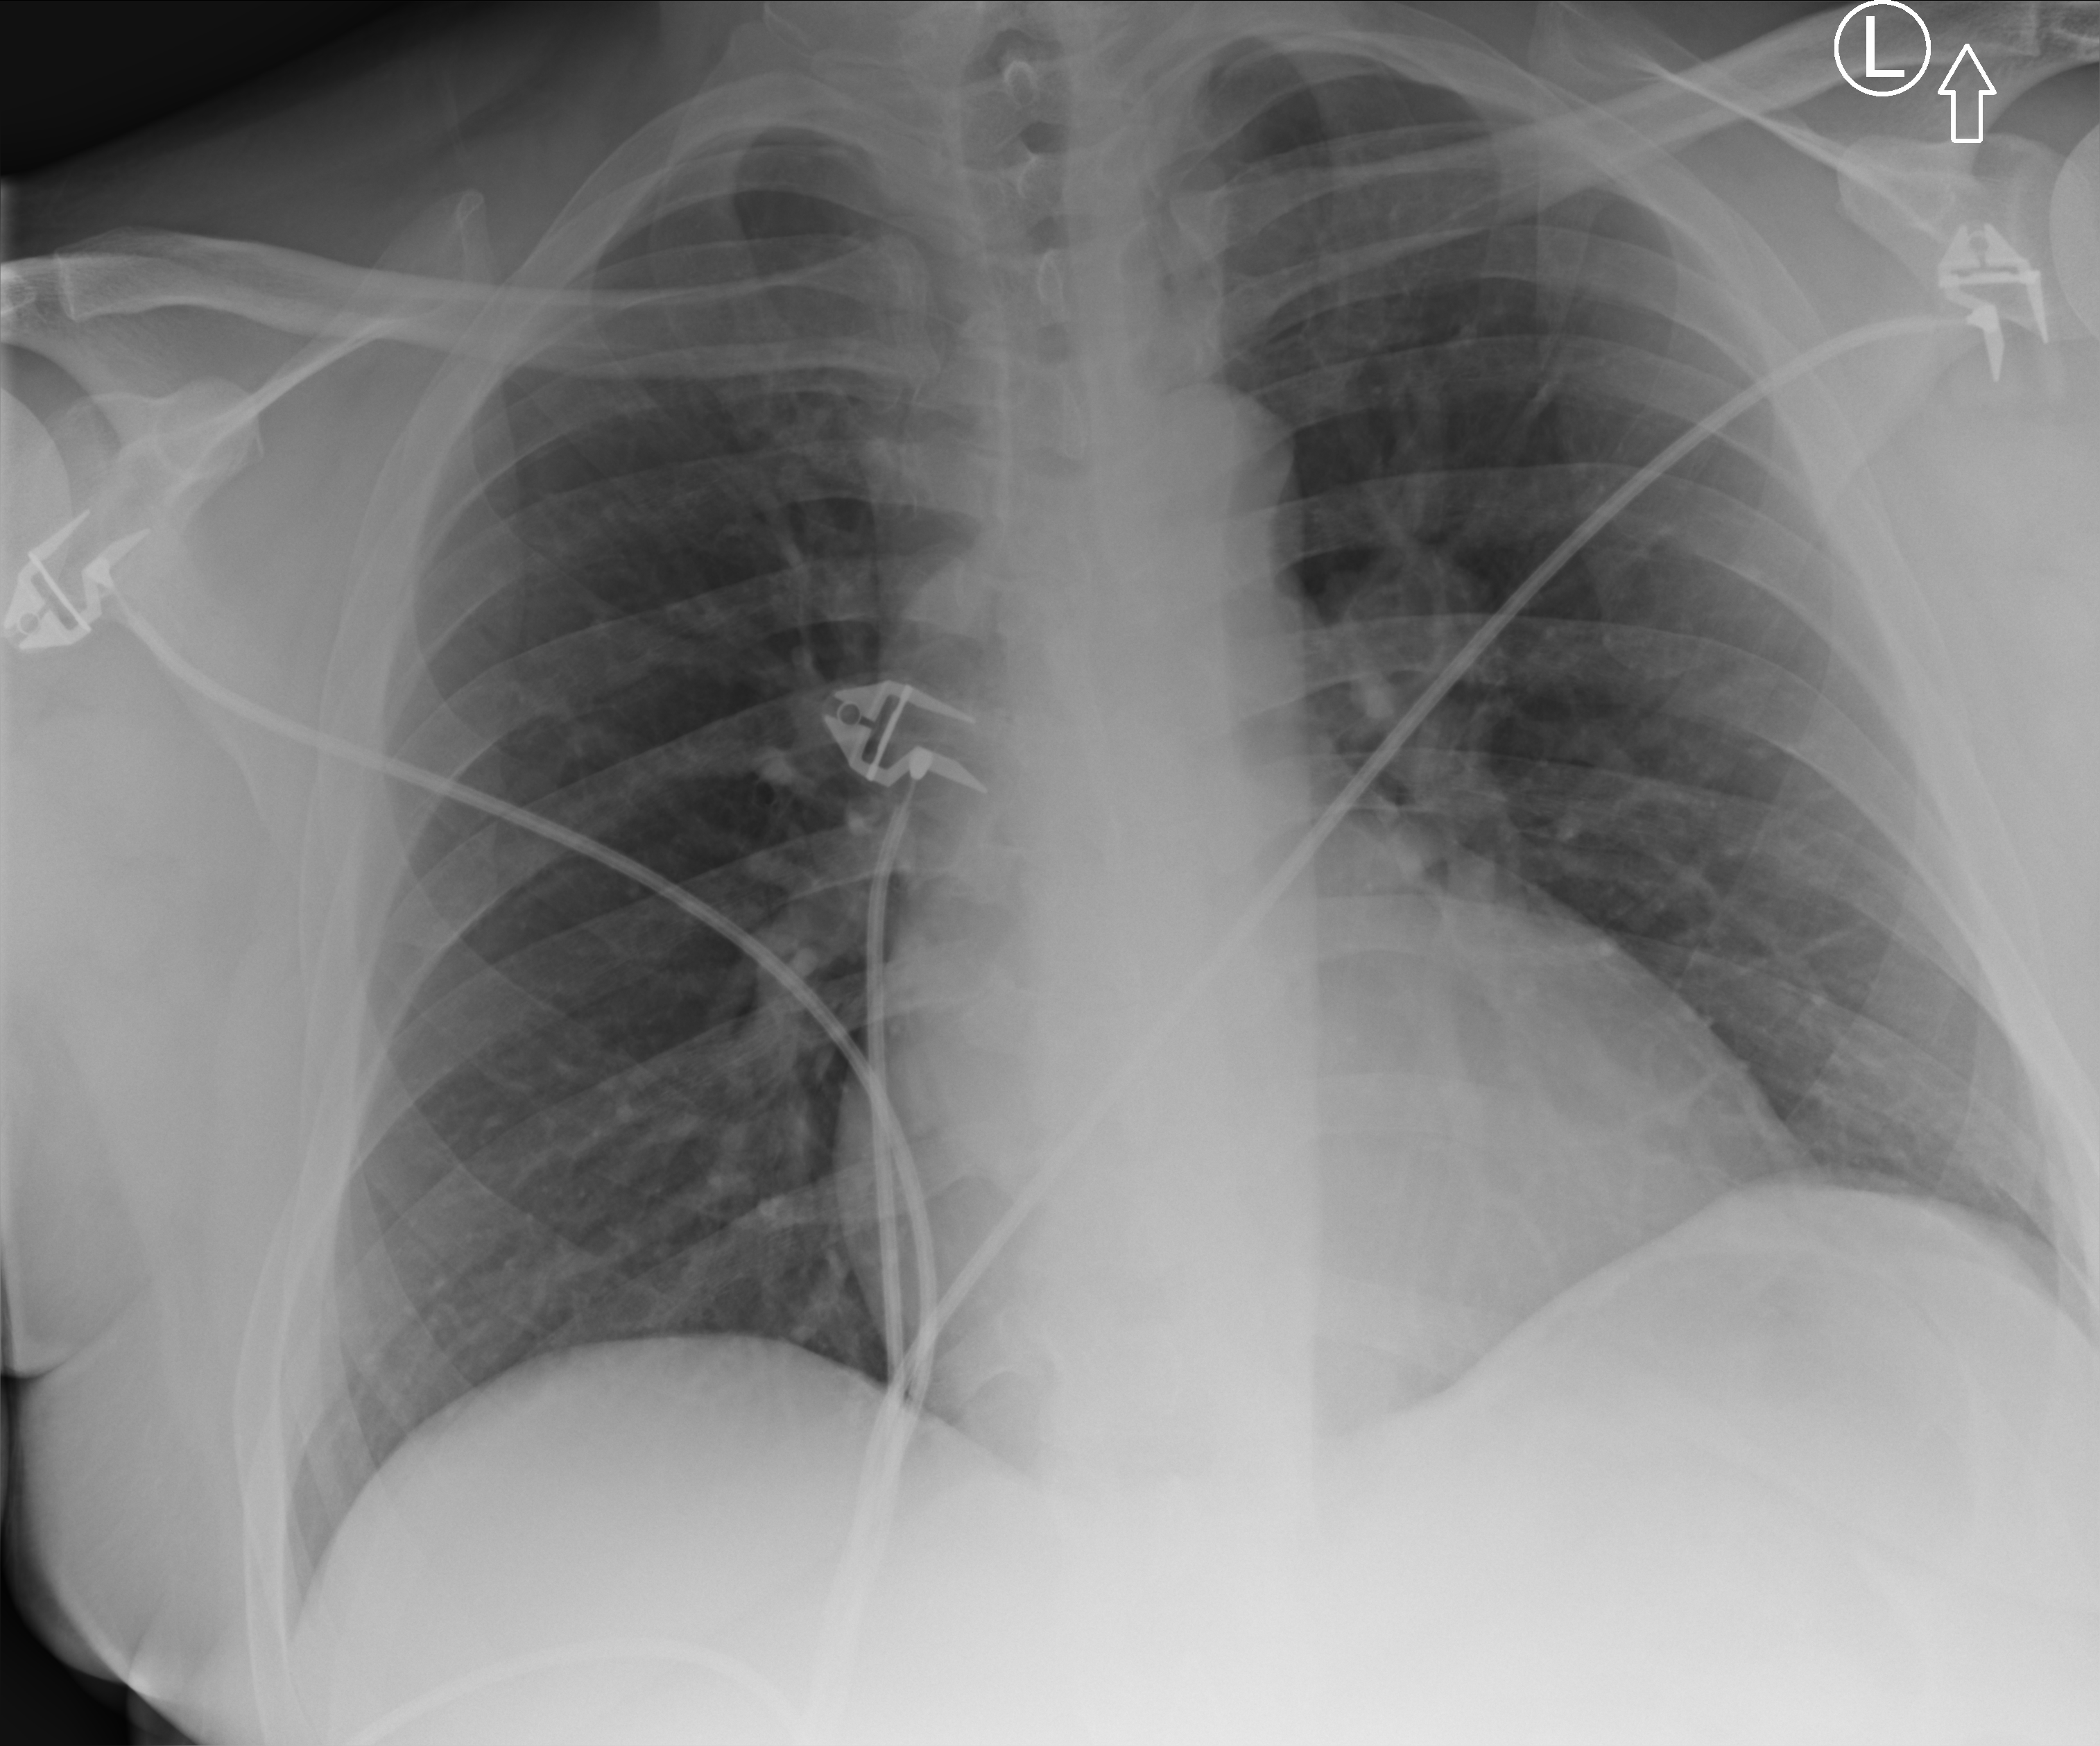
Chest X-ray (portable); anteroposterior (AP) projection. Male patient hospitalised with COVID-19, age 18–59 years.
From the hospital-stay record, not from the radiograph (when in the stay this image was taken is not recorded):
- length of hospital stay: 36 days
- admitted to intensive care during this hospital stay: no
- mechanically ventilated during this hospital stay: no